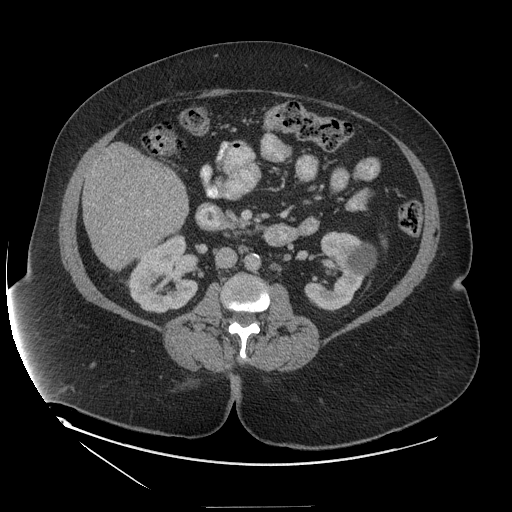
Contrast-enhanced abdominal CT (liver protocol), one axial slice. Position 45 of 127 along the scan axis. Reconstruction kernel STANDARD. 140 kVp. Soft-tissue window (W 400 / L 40 HU). 512 × 512 image matrix, field of view 480 × 480 mm. Case-level facts recorded for this patient, not image findings: diagnosis: hepatocellular carcinoma (patient treated with transarterial chemoembolisation; whether this scan precedes or follows treatment is not stated here); TNM stage (as recorded): Stage-II; Child-Pugh class: A; tumour nodularity: multinodular; tumour size: 3 cm.
Structures marked on this image (semi-automatically segmented with operator editing):
- liver parenchyma outside the tumour (the mass and vessels are separate outlines, so this box may not span the whole liver): bounding box [x1, y1, x2, y2] px = [82, 144, 188, 268]